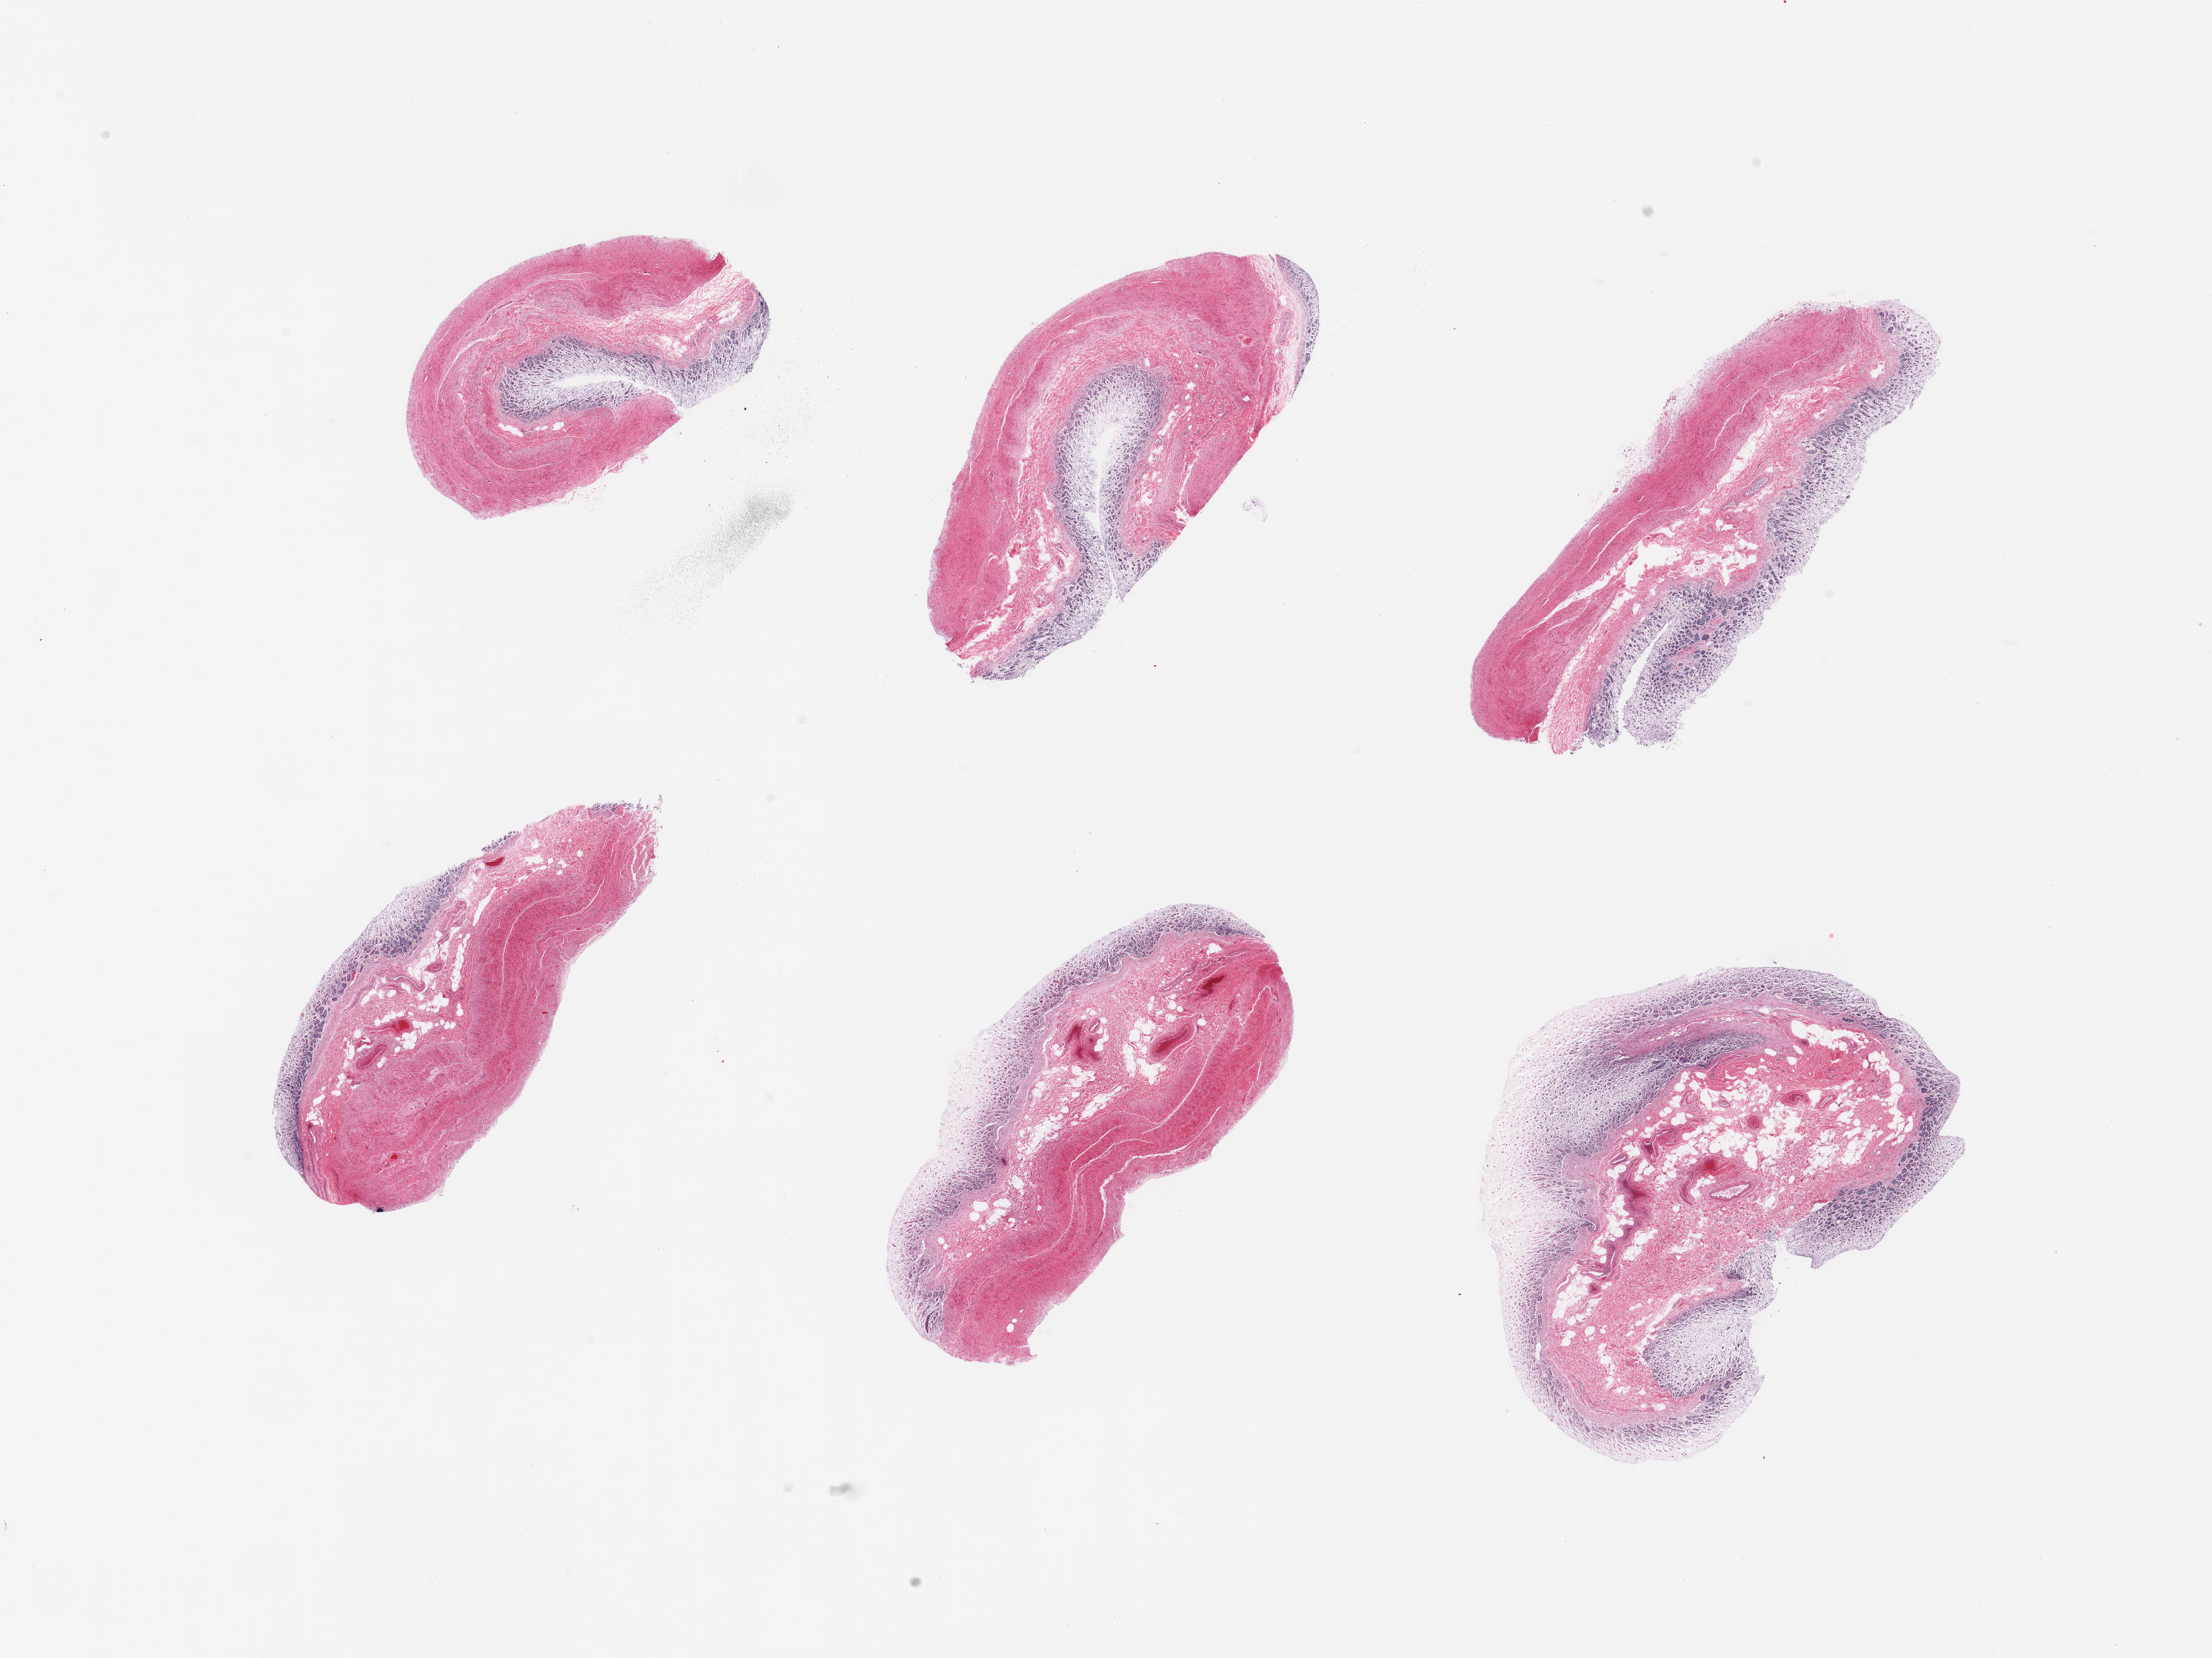
Whole-slide image, haematoxylin and eosin stain, a low-resolution overview of the entire scanned area, about 23.6 x 17.7 mm (from a 20x scan). PAXgene-fixed, paraffin-embedded tissue. Section of stomach (target tissue). Tissue donor sample. Donor sex: female.
Review note (as recorded): 6 pieces.